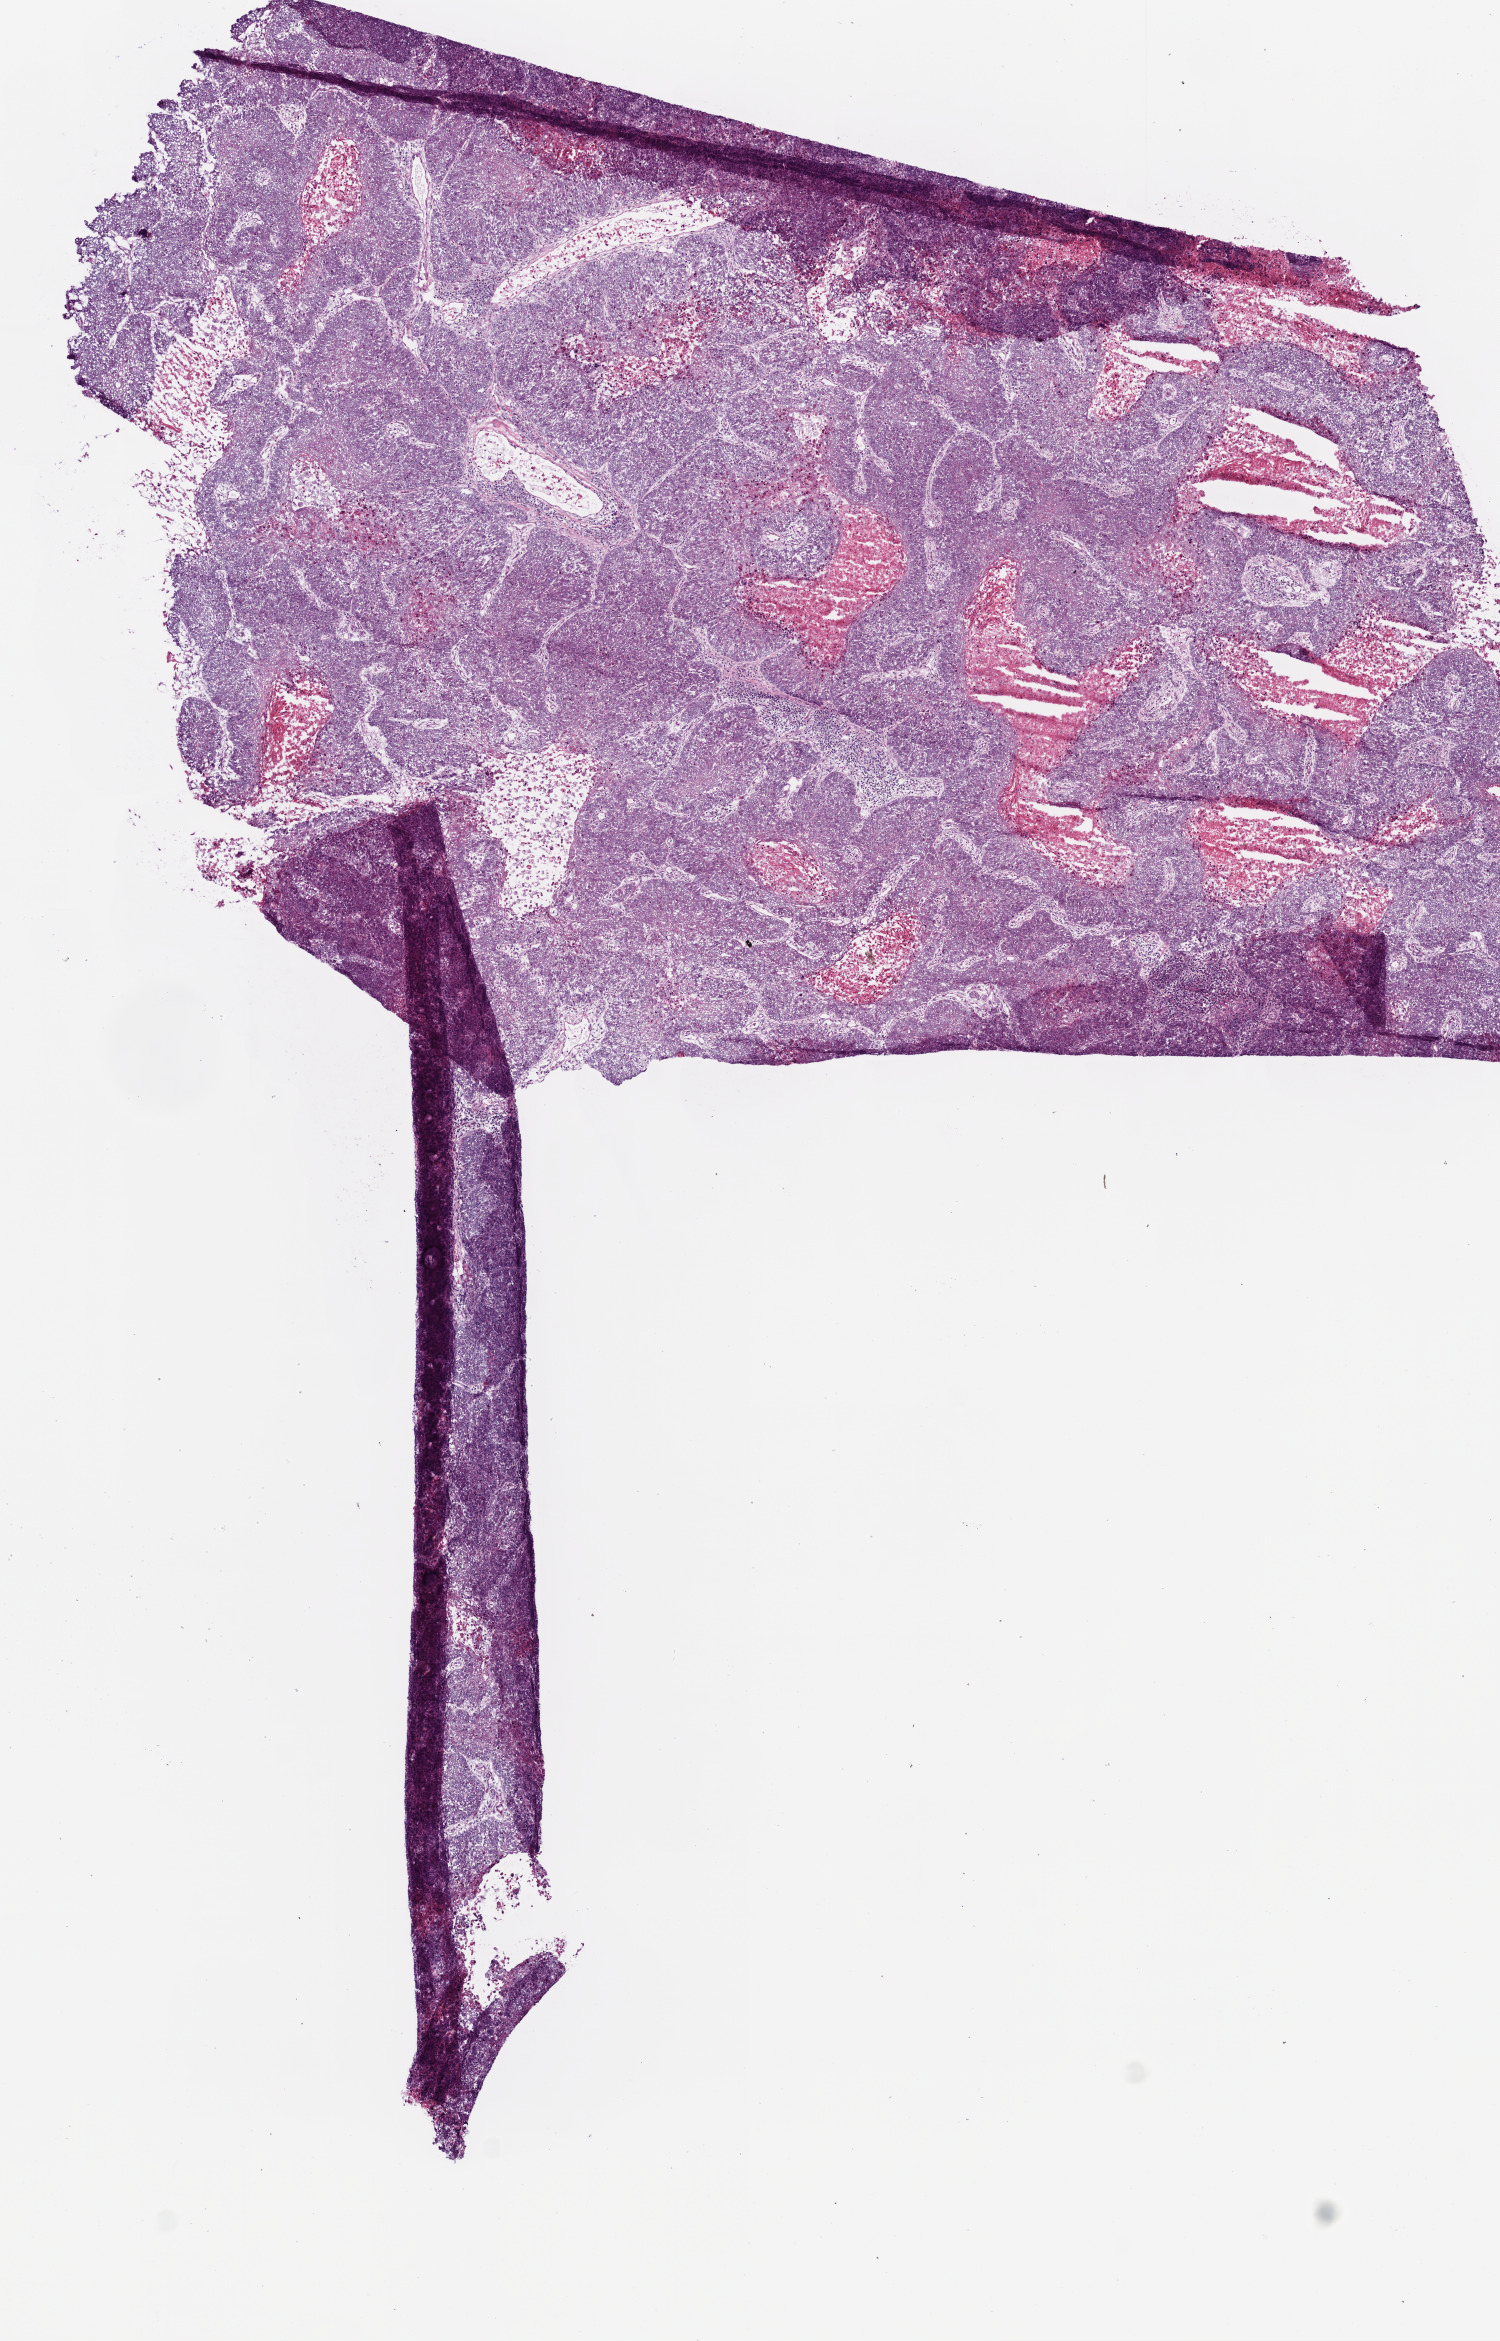
Whole-slide histology image, H&E-stained, low-resolution overview of the scanned area, about 6.0 x 9.4 mm; frozen section from the top of the tissue portion; primary tumour sample from the lung. Male patient; age at initial diagnosis 65 years. Slide review estimates, as recorded: tumour cells 77%, tumour nuclei 90%, normal cells 0%, stromal cells 3%, necrosis 20%.
Pathologic diagnosis: Basaloid squamous cell carcinoma (upper lobe, lung). AJCC pathologic stage: IIIB. Laterality: right.